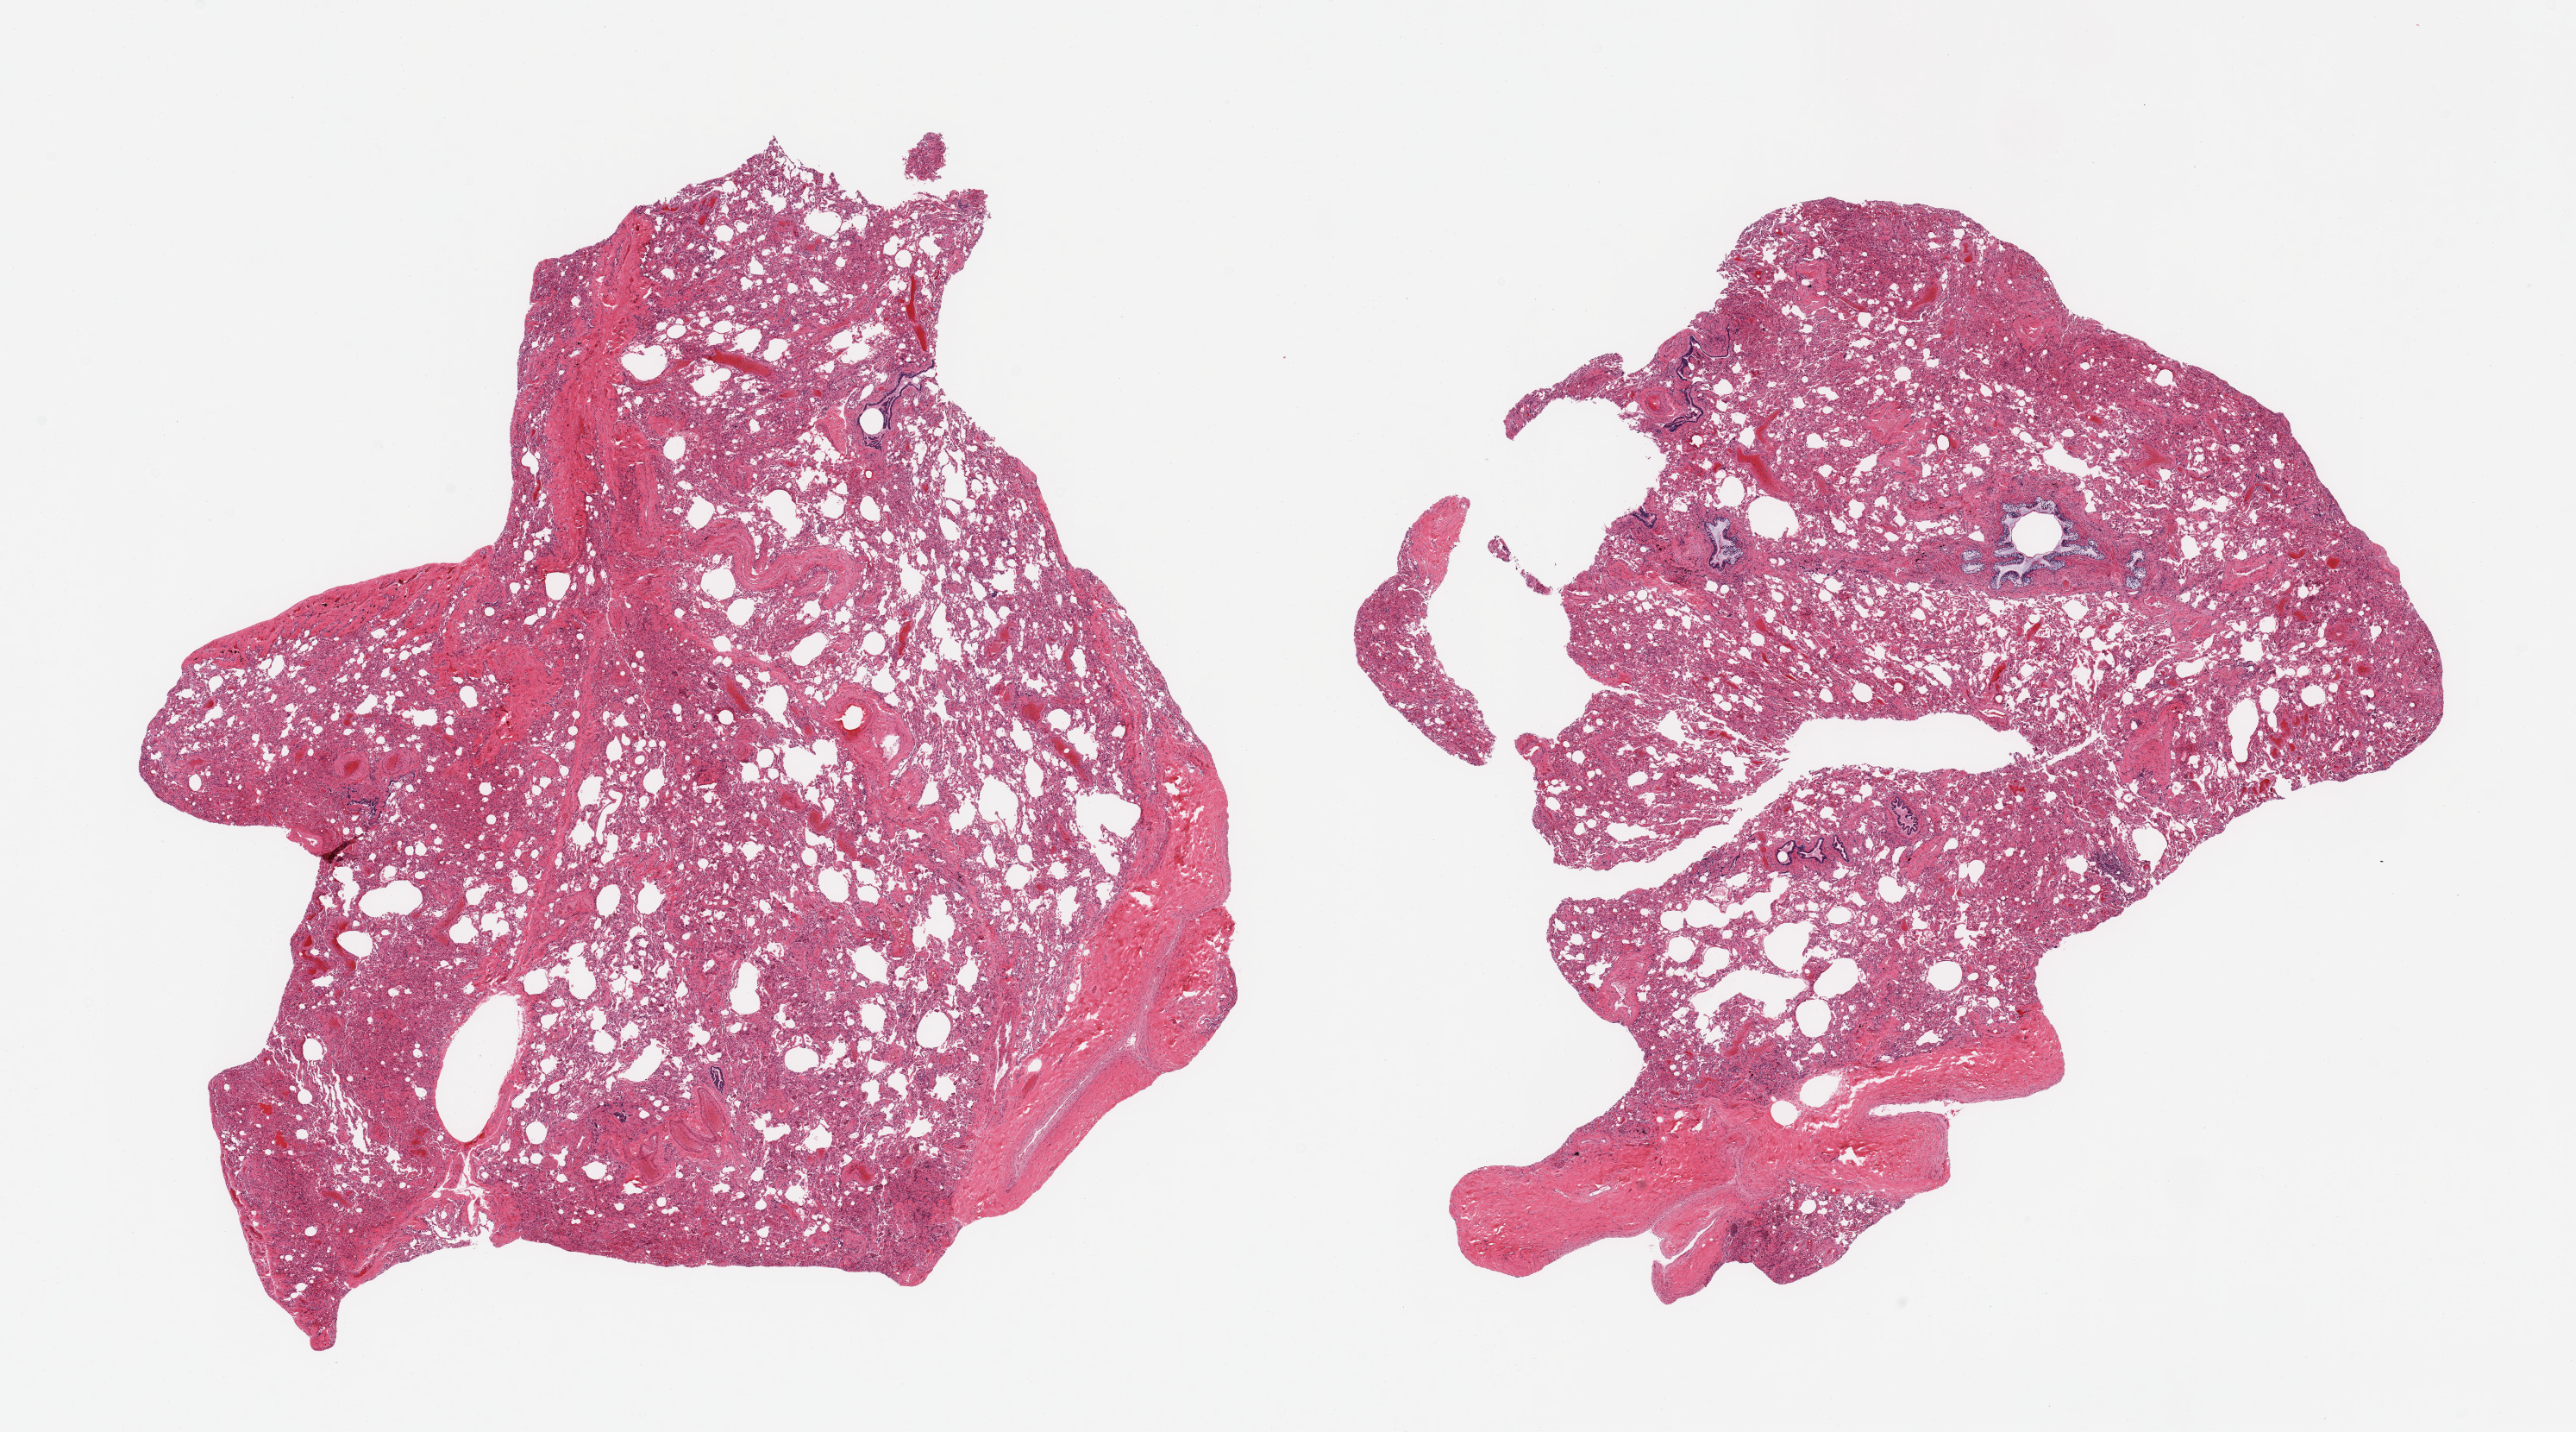
Digitized H&E-stained section, a low-resolution overview of the entire scanned area, about 23.6 x 13.1 mm (slide scanned at 20x), PAXgene-fixed paraffin-embedded (PFPE) section, target tissue: lung, donor tissue sample. Male donor.
Pathologist's review note for this sample: 2 pieces; atelectasis, focal smooth muscle hypertrophy and increased mucosal goblet cells.